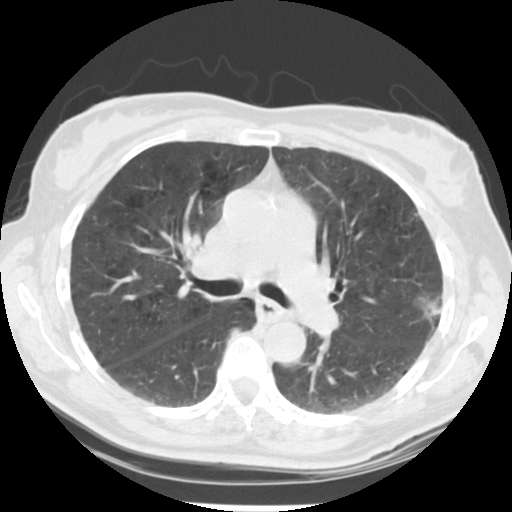
Chest CT (low-dose screening protocol), one axial image; second annual screen; lung window (W 1500 / L -600 HU); 2.5 mm slice thickness; slice 134 of 223 in the series. Female, age 61 years at enrolment. Current smoker at enrolment.
Expert reader's lesion annotation, box from (x=405, y=280) to (x=464, y=341) px. The exam's reader record, not a measurement of the box and not confirmed to be the same lesion: non-calcified nodule or mass ≥4 mm, left upper lobe, 15 × 15 mm, poorly defined margins, mixed attenuation, pre-existing on the prior screen: no. Participant outcome: lung cancer diagnosed 152 days after this screen — bronchiolo-alveolar adenocarcinoma, NOS, left upper lobe, well differentiated (G1), stage IA (AJCC 6th edition), 11 mm at pathology.